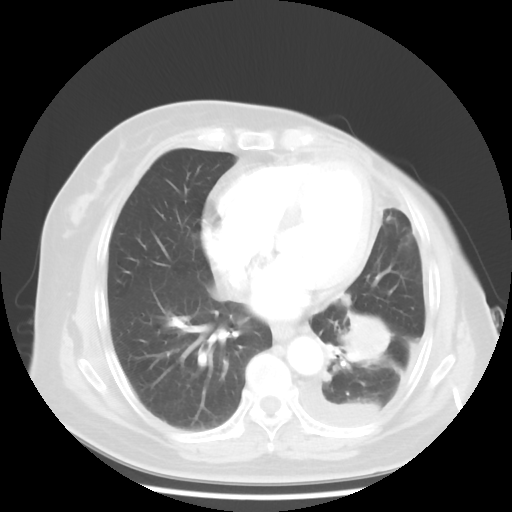
Chest CT, one axial slice; slice 17 of 48 in the series (ordered by position); 120 kVp; lung window (W 1500 / L -600 HU); 512 × 512 image matrix, field of view 360 × 360 mm. Female patient, age 63 years. Case-level facts recorded for this patient, not image findings: clinical TNM (as recorded): T2 N0 M1.
Structures marked on this image (bounding box drawn by a radiologist):
- lung tumour (recorded histology: adenocarcinoma): bounding box (x1, y1, x2, y2) in pixels: (336, 303, 403, 371)